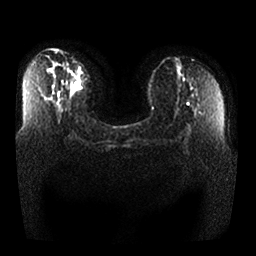
Breast MRI, one axial slice; slice 13 of 25 in the series (ordered by position); diffusion-weighted series; image 2 of 4 stored at this slice position (different b-values; order by instance number); 1.5 T; 256 × 256 image matrix. Female patient.
Annotated regions visible in this slice (outlined manually by an expert reader):
- tumour on diffusion-weighted imaging: bounding box [x1, y1, x2, y2] px = [73, 79, 80, 86]